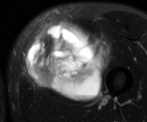
MRI of an extremity soft-tissue mass, one axial slice; position 24 of 52 along the scan axis; T2-weighted fat-saturated; MR volume resampled by the dataset authors to the PET/CT grid (not the native acquisition matrix); 3.27 mm slice thickness; 147 × 122 image matrix. Male patient. From the clinical record (not read from this slice): histological type: pleiomorphic liposarcoma; grade: high; site of the primary tumour: left thigh.
Outlined on this slice (expert contour drawn on MRI and transferred to this co-registered scan by the dataset authors):
- gross tumour volume including surrounding oedema: bounding box <23,19,111,102> (left, top, right, bottom; pixels)
- gross tumour volume (mass): <25,19,106,102>